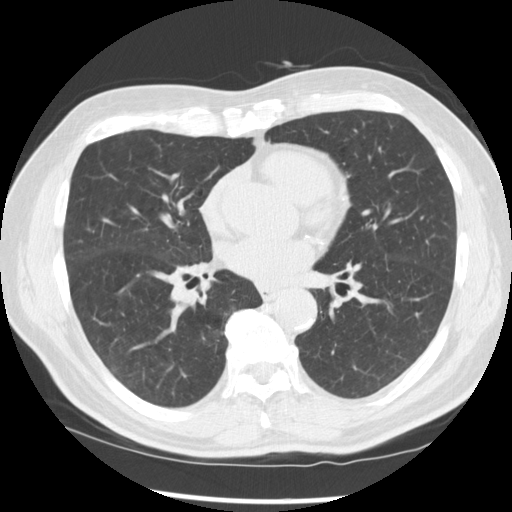
Low-dose screening chest CT, one axial slice; position 134 of 277 along the scan axis; reconstruction kernel STANDARD; 120 kVp; lung window (W 1500 / L -600 HU); 2.5 mm slice thickness; 512 × 512 image matrix, field of view 365 × 365 mm.
Outlined on this slice (manually delineated by an expert):
- lesion 1 (tumor, middle lobe of right lung): bounding box [x1, y1, x2, y2] px = [170, 285, 197, 306]